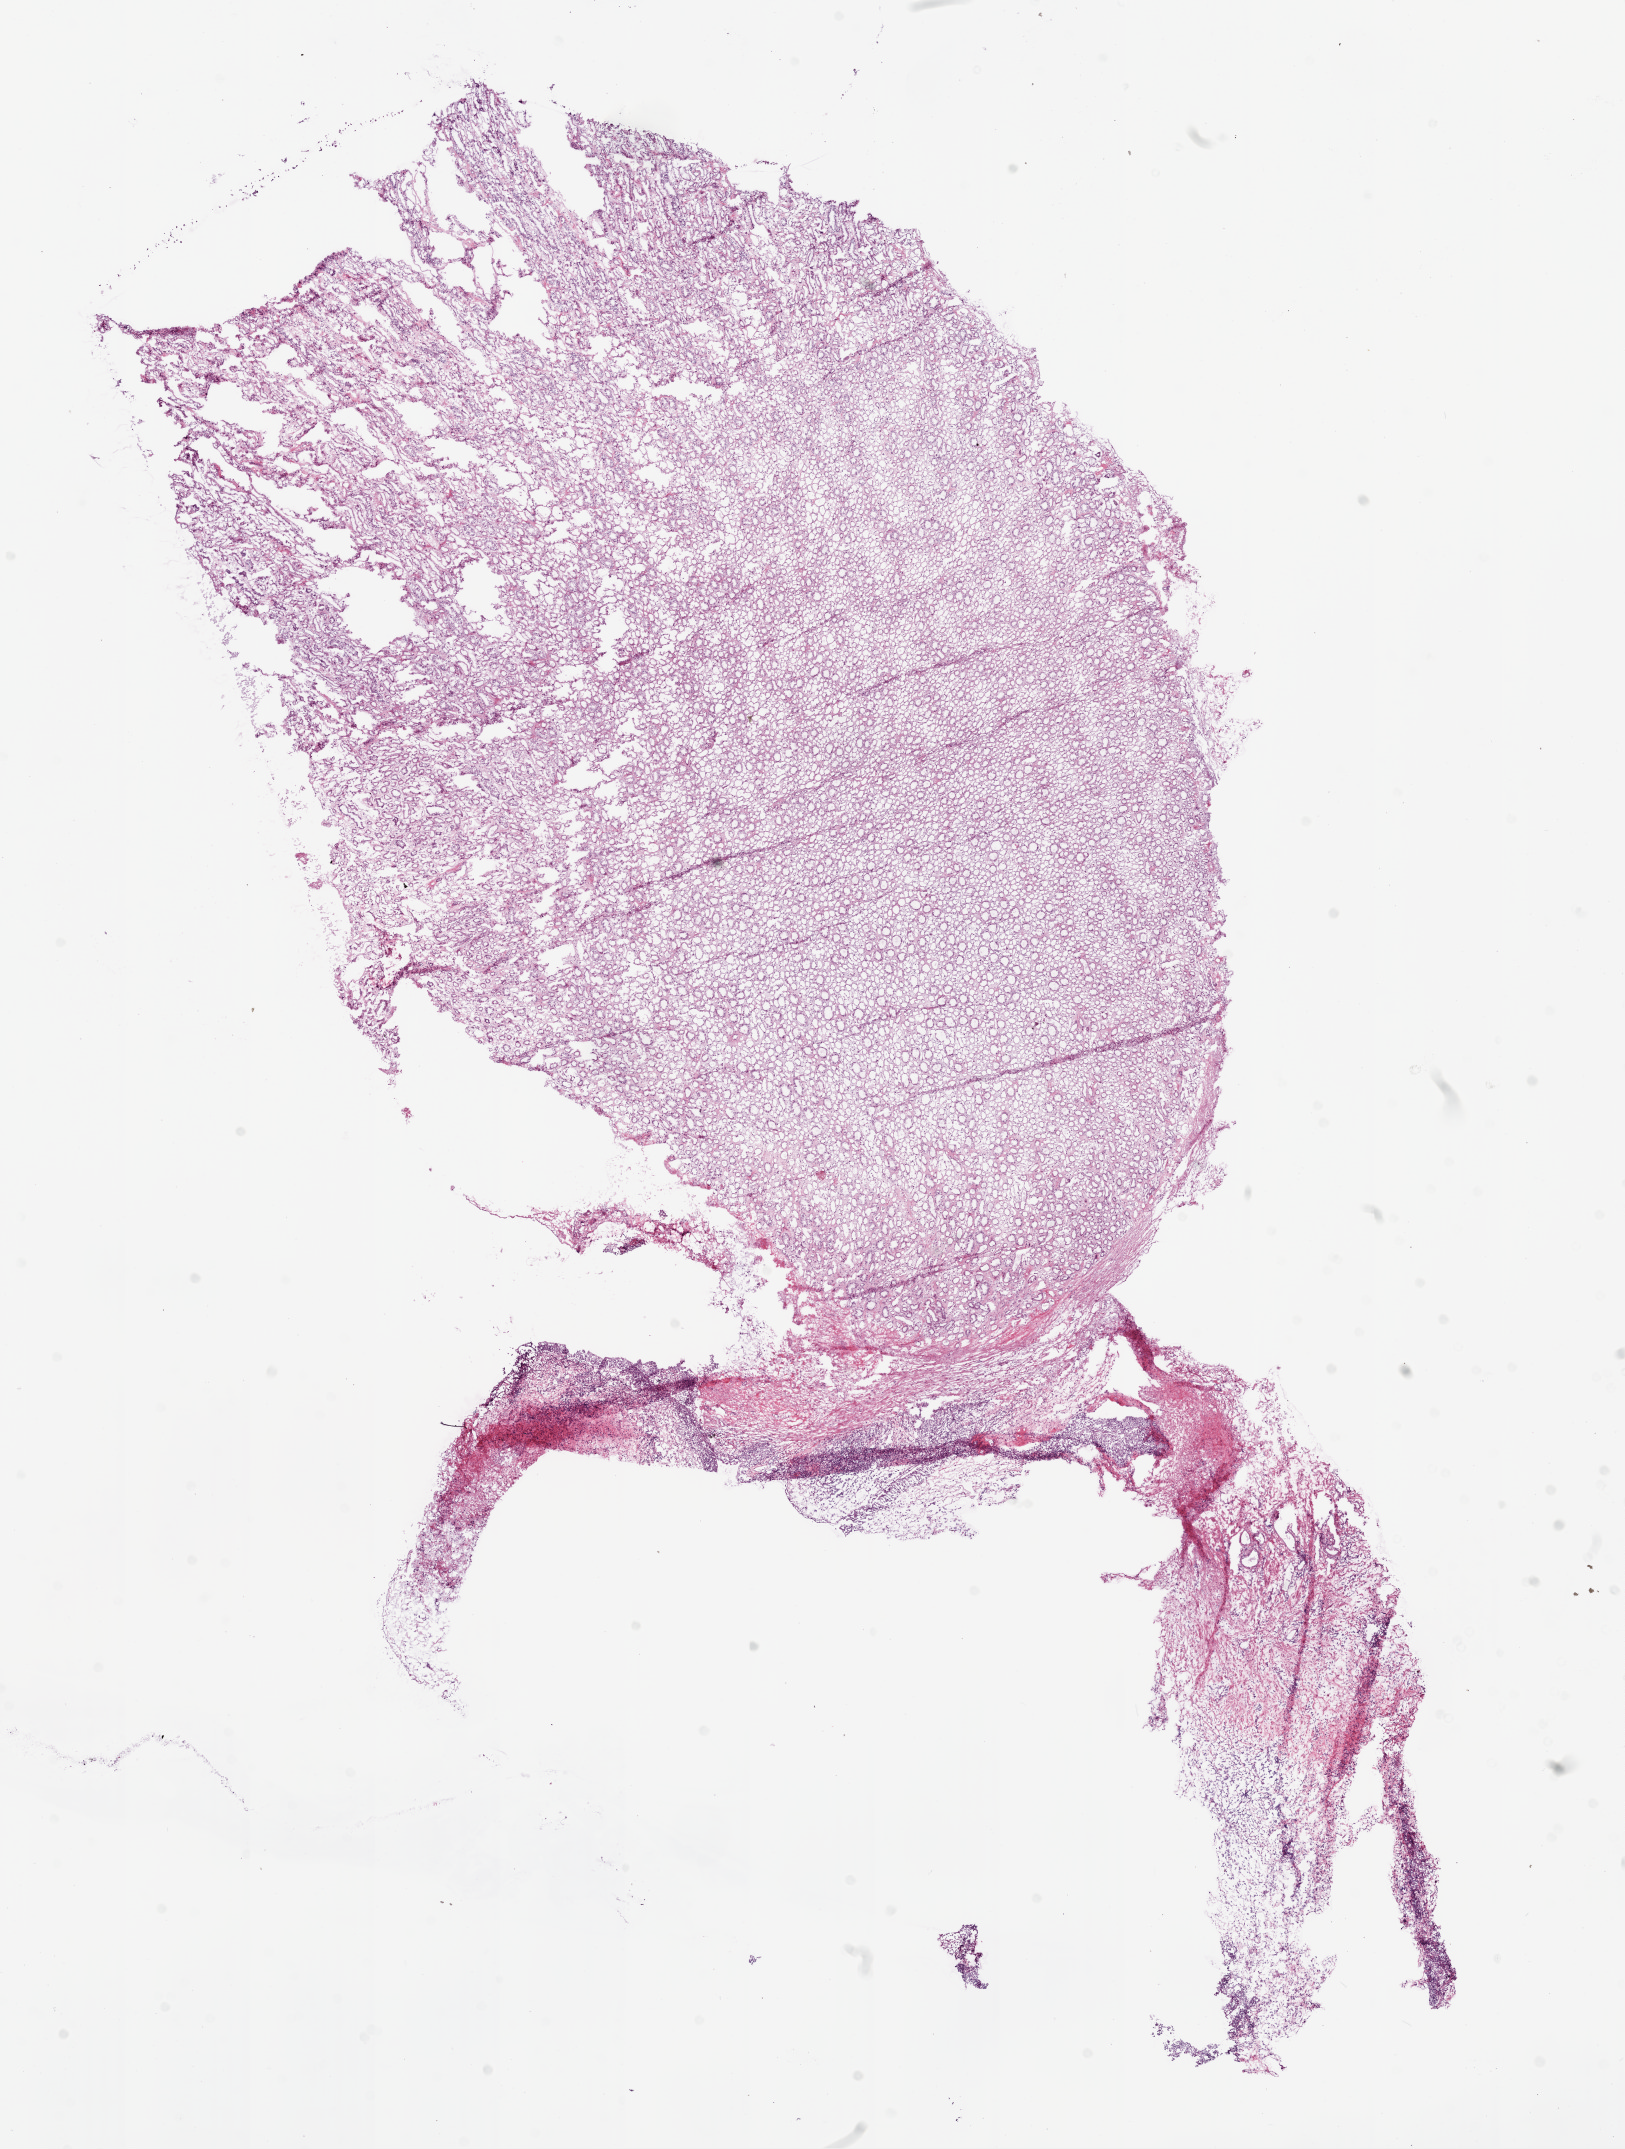
H&E whole-slide image, whole scanned area (about 13.0 x 17.2 mm) shown as a low-resolution overview; frozen section from the bottom of the tissue portion; solid tissue normal (non-tumour tissue) sample from the kidney. Male patient; age at initial diagnosis 68 years.
This section: solid tissue normal sample (biorepository sample class). Patient diagnosis: Clear cell adenocarcinoma, NOS.